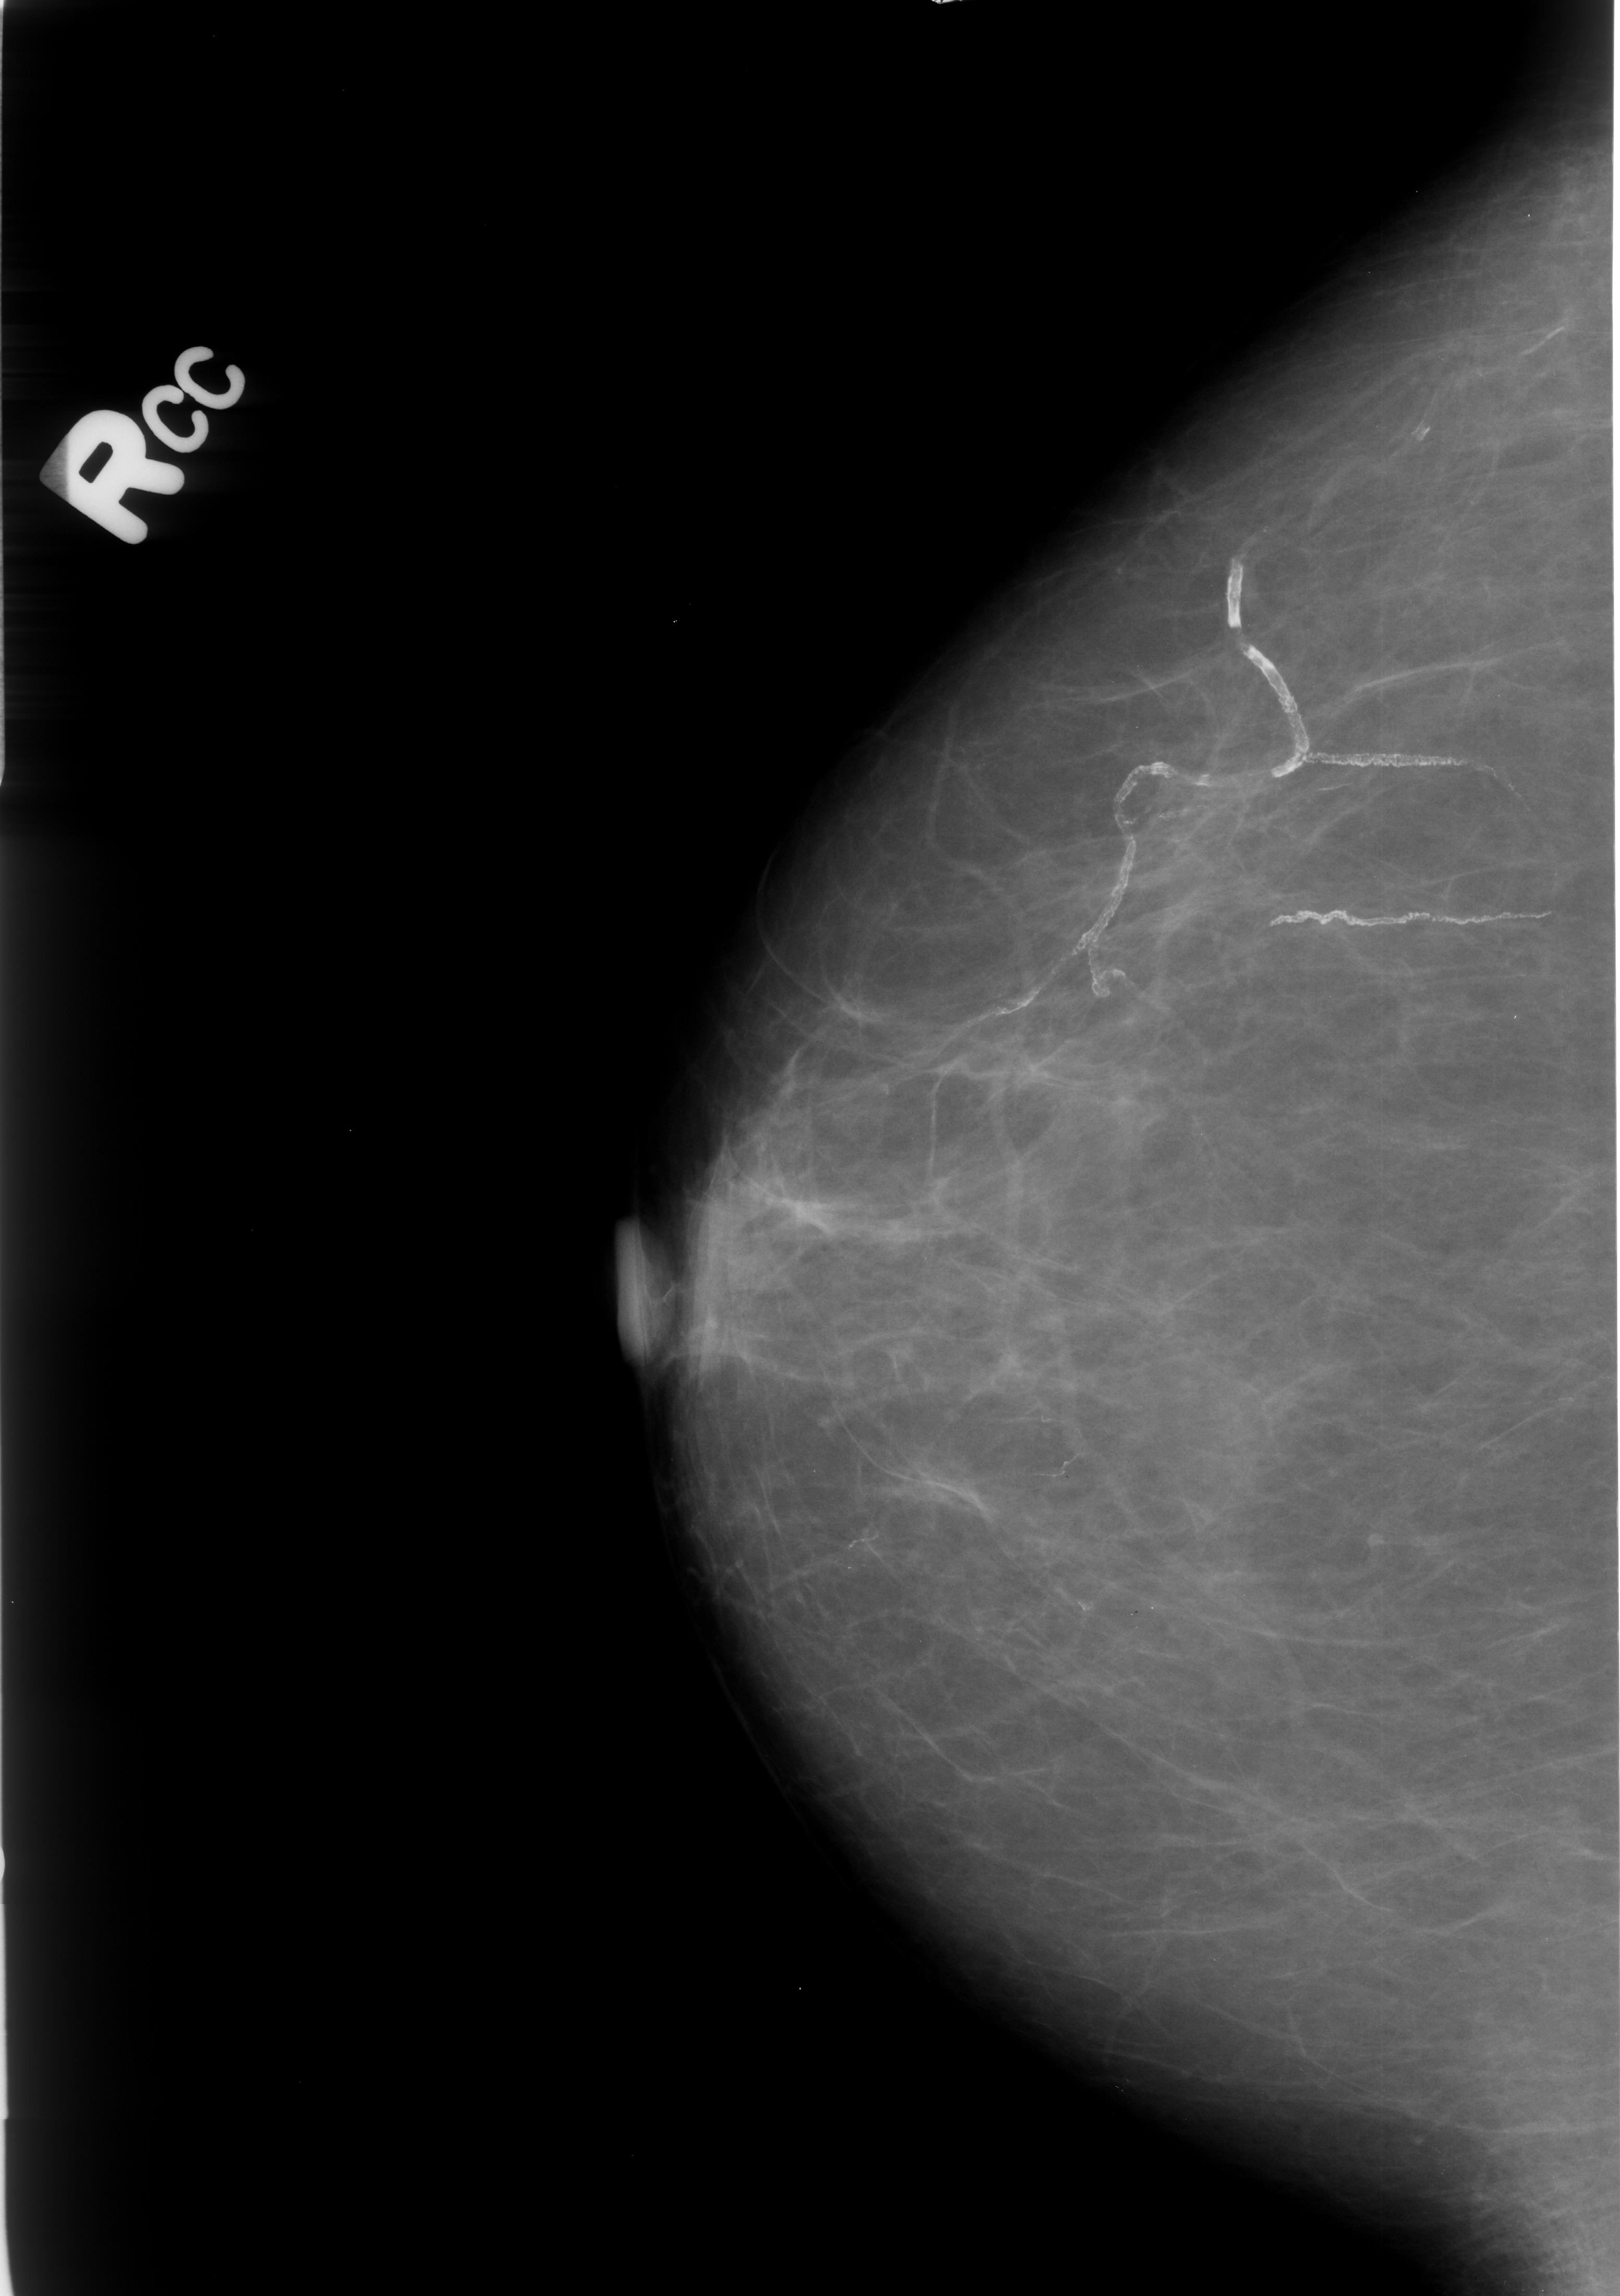
Digitized screen-film mammogram; right breast; CC view; breast composition: almost entirely fatty (BI-RADS density category 1 of 4).
- Radiologist-marked abnormalities on this image: Finding 1 of 5: calcifications, morphology vascular; BI-RADS assessment category 2; subtlety rating 4 on a 1 (subtle) to 5 (obvious) scale; benign; no additional work-up was recommended (benign without callback).
- Finding 2 of 5: calcifications, morphology vascular; BI-RADS assessment category 2; subtlety rating 4 on a 1 (subtle) to 5 (obvious) scale; benign; no additional work-up was recommended (benign without callback).
- Finding 3 of 5: calcifications, morphology fine linear branching; BI-RADS assessment category 2; benign; no additional work-up was recommended (benign without callback).
- Finding 4 of 5: calcifications, morphology fine linear branching; BI-RADS assessment category 2; subtlety rating 4 on a 1 (subtle) to 5 (obvious) scale; benign without callback (not worked up further).
- Finding 5 of 5: calcifications, morphology fine linear branching; BI-RADS assessment category 2; subtlety rating 4 on a 1 (subtle) to 5 (obvious) scale; benign; no additional work-up was recommended (benign without callback).